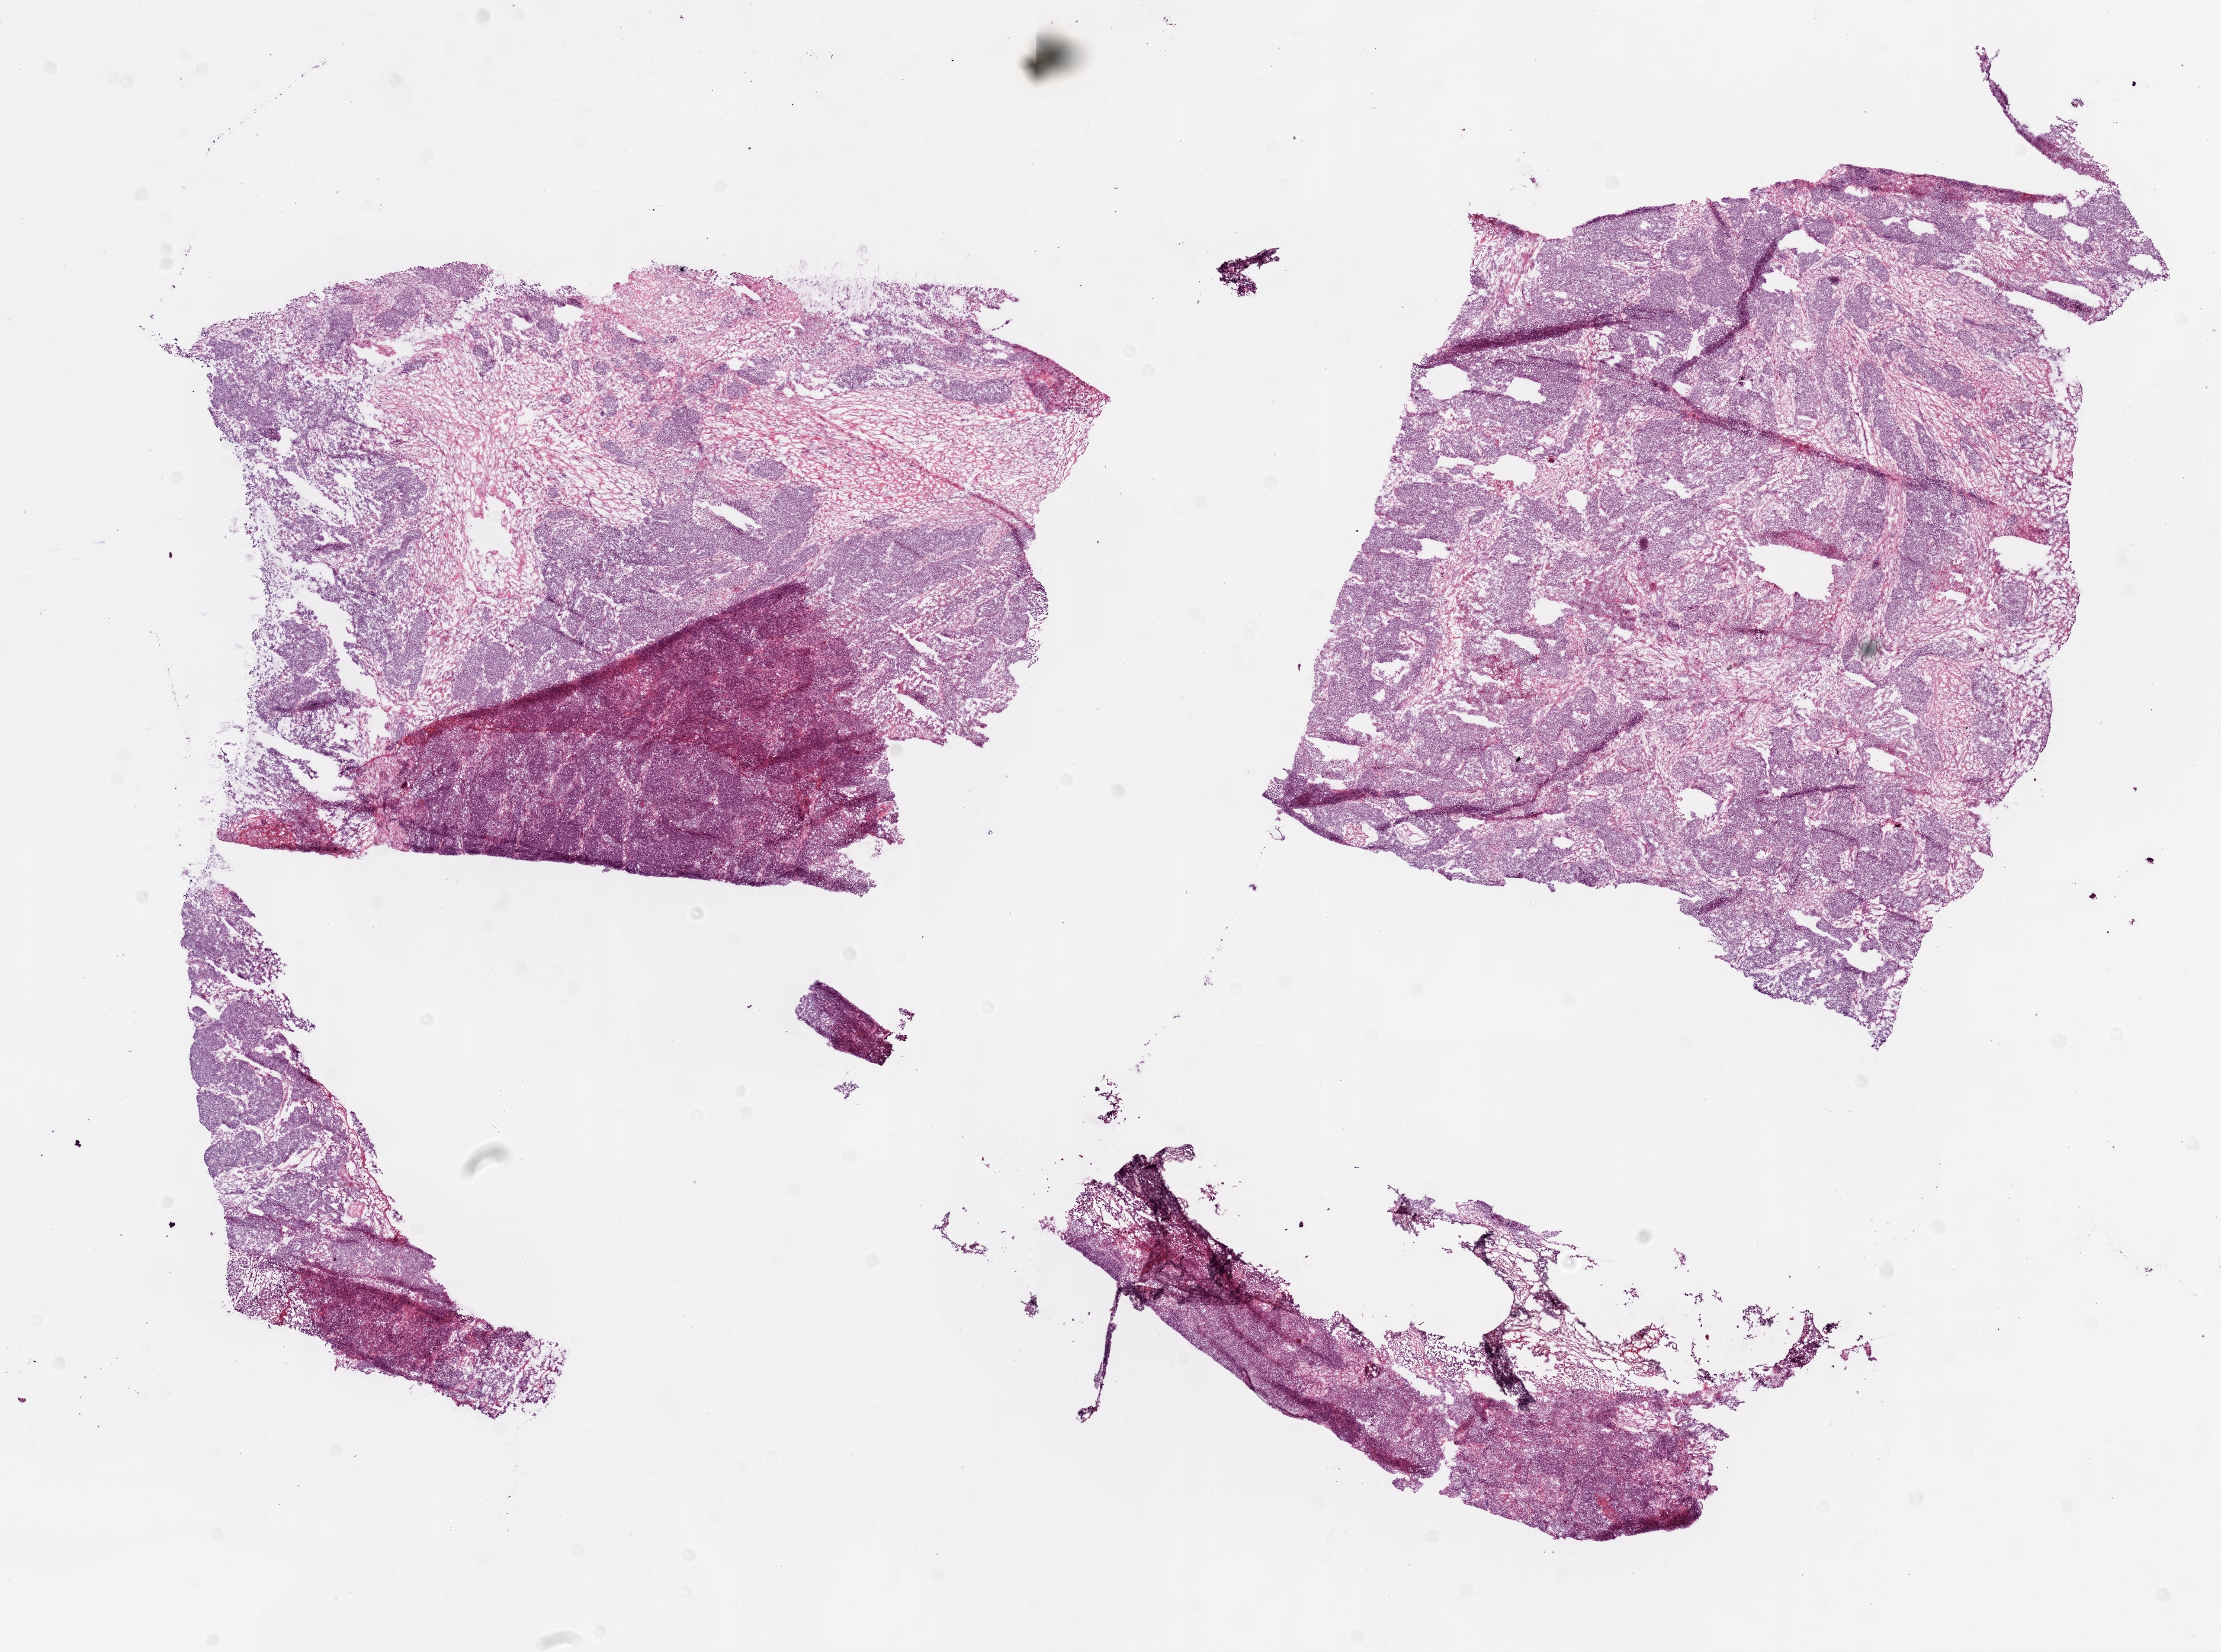
H&E whole-slide image, whole scanned area (about 15.0 x 11.2 mm, acquisition: 20x scan) shown as a low-resolution overview, frozen section from the bottom of the tissue portion, primary tumour sample from the ovary. Female, age 52 years at initial diagnosis. Histologic grade: G3 (poorly differentiated). Composition of this section per pathologist review: tumour cells 85%, tumour nuclei 90%, normal cells 2%, stromal cells 8%, necrosis 5%.
Pathologic diagnosis: Serous cystadenocarcinoma, NOS. FIGO stage: IIIB.